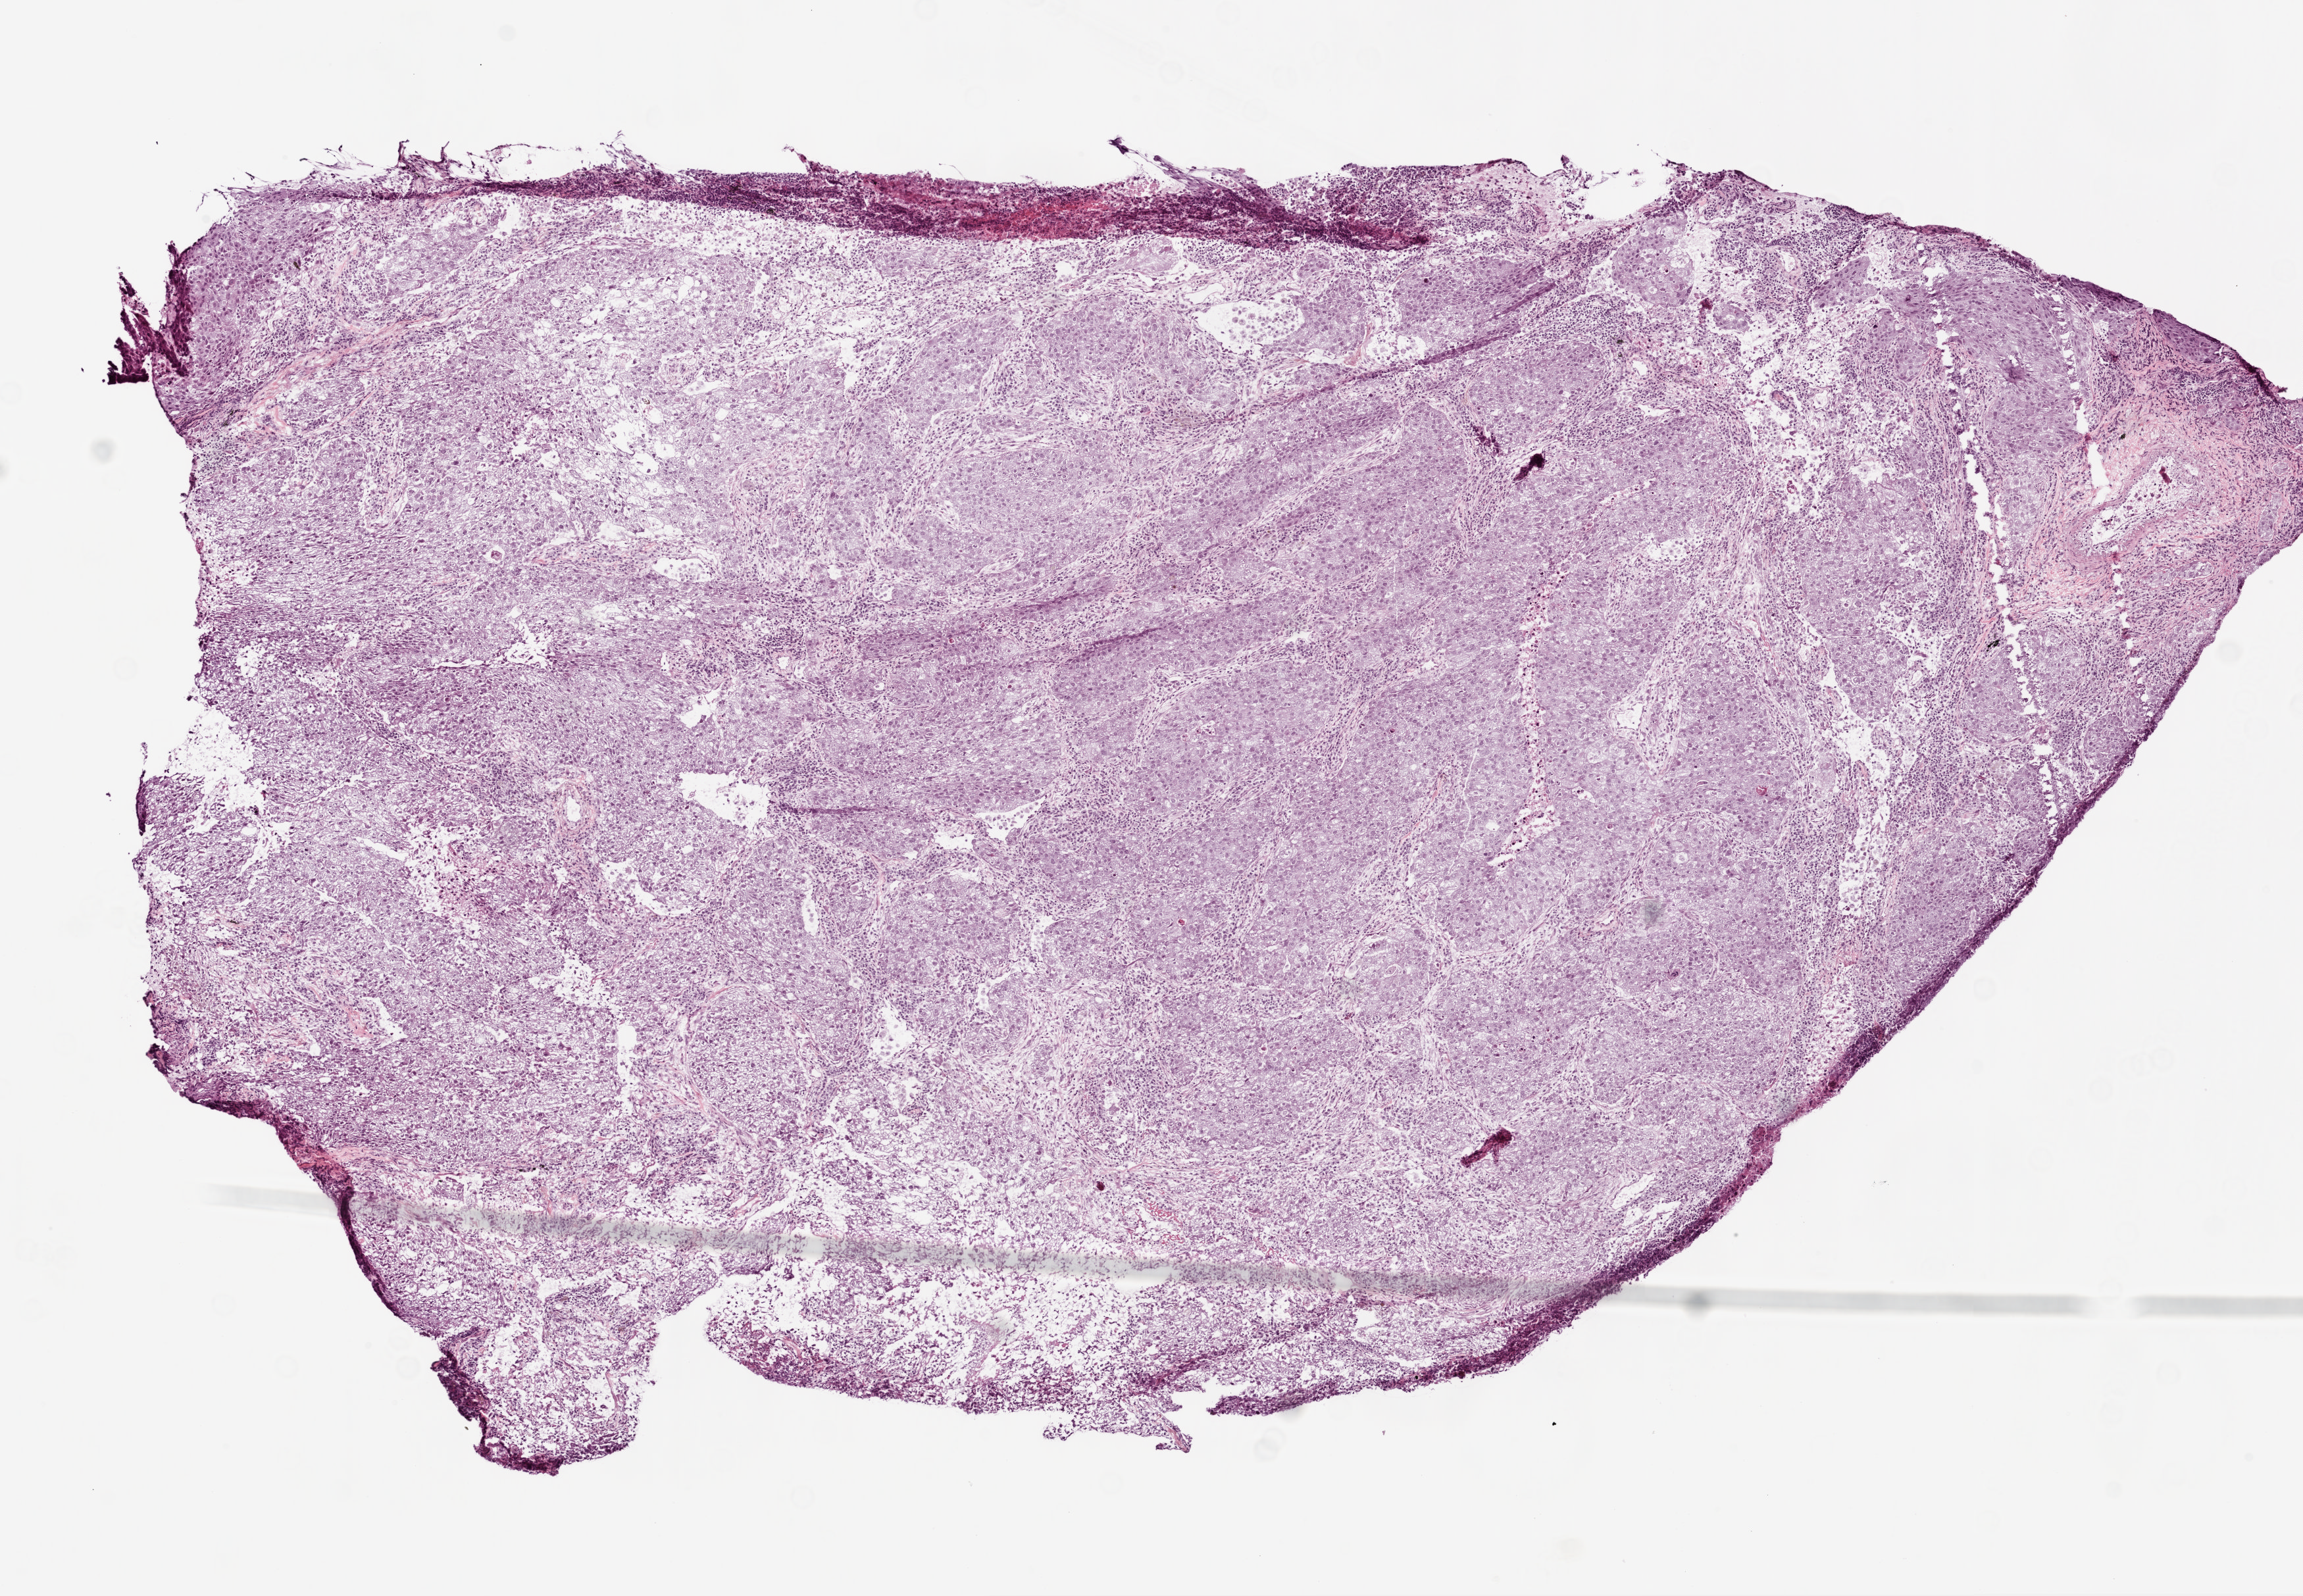
Hematoxylin and eosin (H&E) stained whole-slide image — low-resolution overview of the scanned area, about 7.0 x 4.9 mm. Frozen section from the top of the tissue portion. Sample: primary tumour, lung. Patient: female, age at initial diagnosis 66 years.
Pathologic diagnosis: Squamous cell carcinoma, NOS.